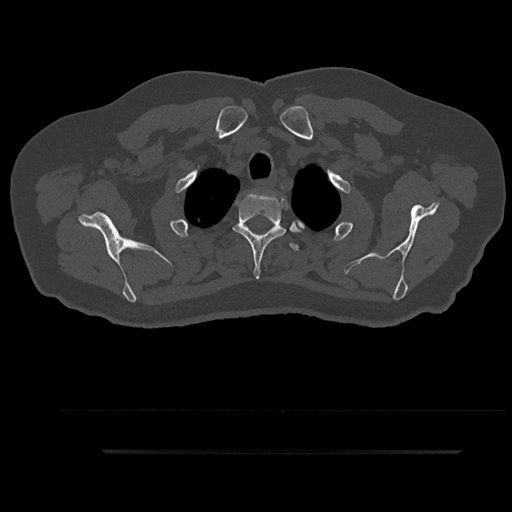
CT including the spine, one axial slice; slice 754 of 797 in the series (ordered by position); reconstruction kernel Br40s/3; 120 kVp; bone window (W 1800 / L 400 HU); 0.5 mm slice thickness; 512 × 512 image matrix, field of view 432 × 432 mm. Patient: male, 63 years. Case-level facts recorded for this patient, not image findings: primary cancer: renal.
Annotated regions visible in this slice (semi-automatically segmented with operator editing):
- T2 vertebra: bounding box (x1, y1, x2, y2) in pixels: (233, 192, 303, 279)
- T3 vertebra: (218, 222, 299, 251)